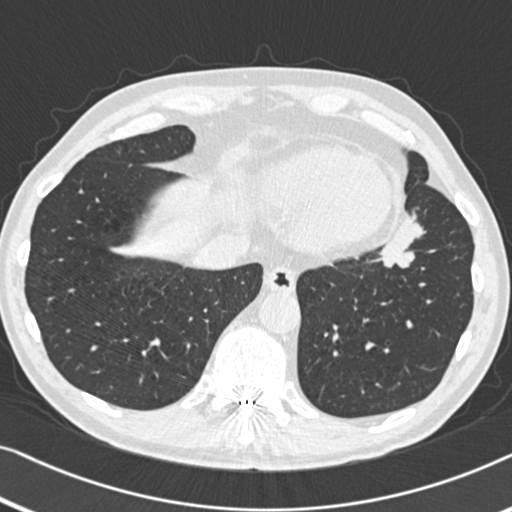
Low-dose screening chest CT, one axial slice. Position 125 of 383 along the scan axis. Lung window (W 1500 / L -600 HU). 1 mm slice thickness. 512 × 512 image matrix.
Outlined on this slice (outlined manually by an expert reader):
- lesion 1 (tumor, upper lobe of left lung): bounding box <380,212,425,268> (left, top, right, bottom; pixels)